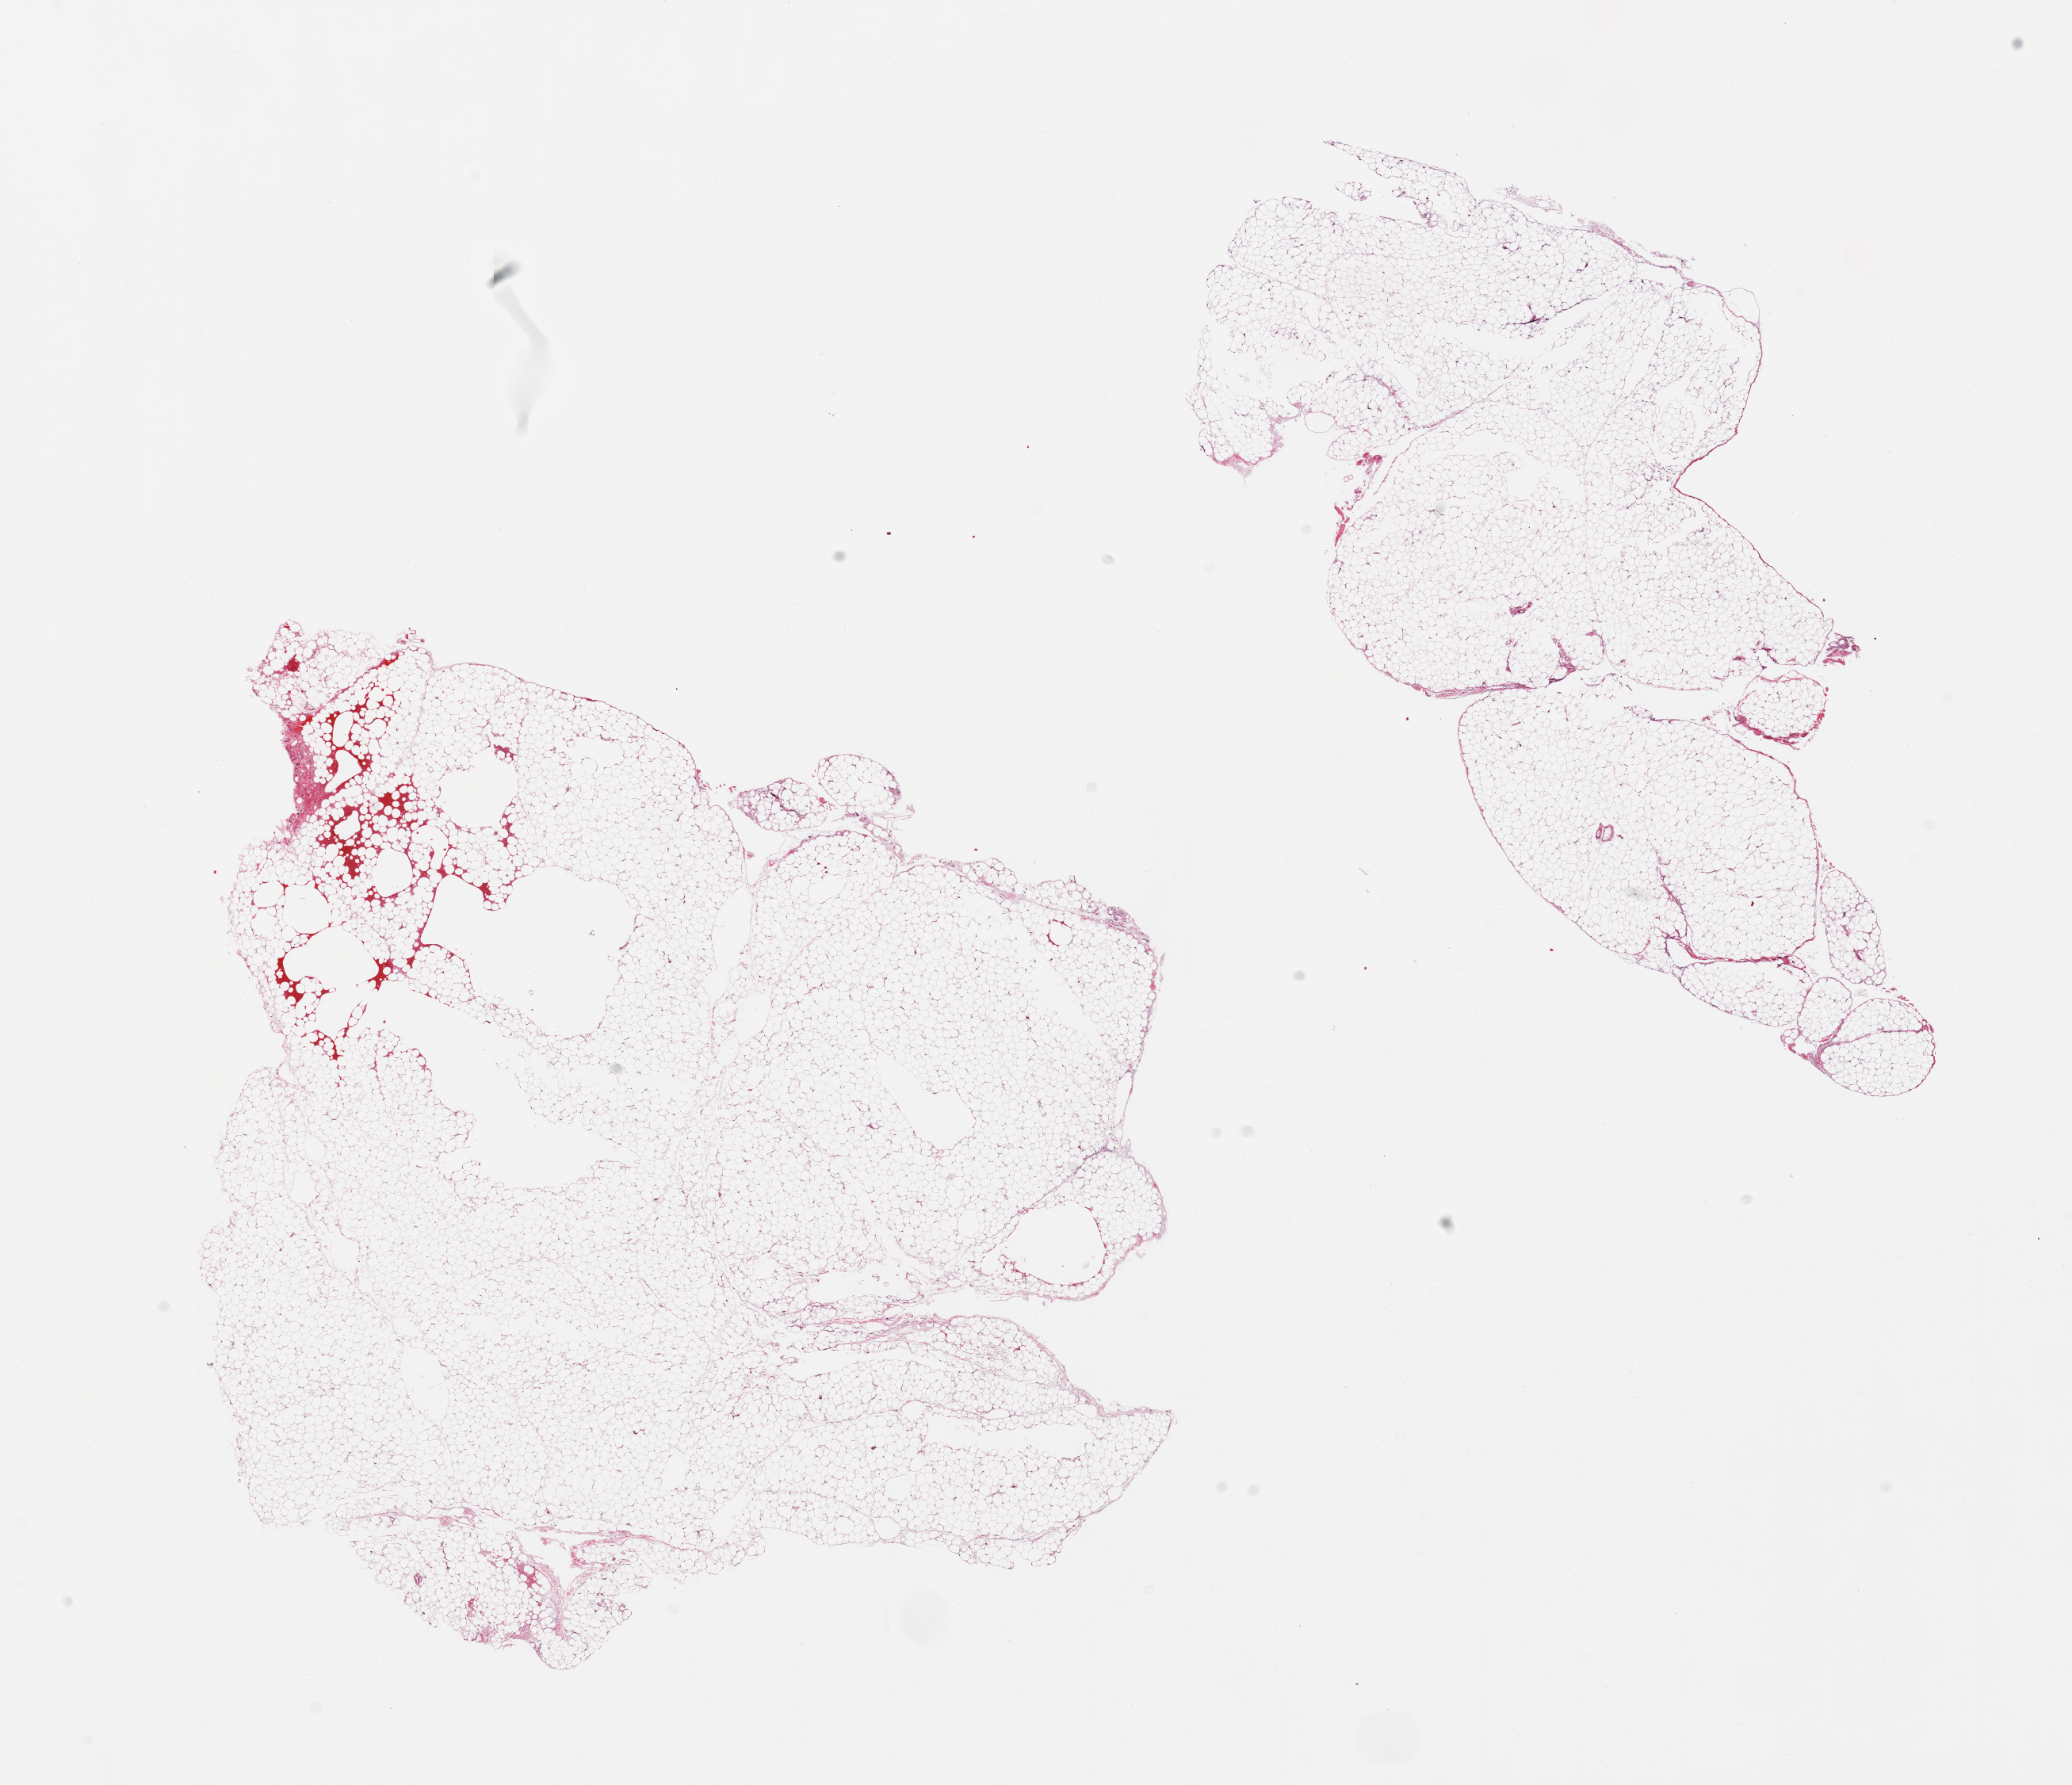
Whole-slide image, H&E stain, brightfield, a low-resolution overview of the entire scanned area, about 20.7 x 17.8 mm (from a 20x scan), PAXgene-fixed paraffin-embedded (PFPE) section, target tissue: omentum, donor tissue sample.
Pathologist's review note for this sample: 2 pieces; focal fresh mild hemorrhage.